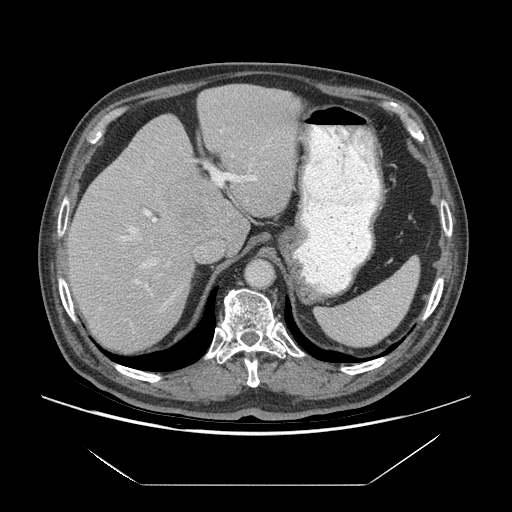
Contrast-enhanced abdominal CT (liver protocol), one axial slice. Slice 48 of 75 in the series (ordered by position). Reconstruction kernel STANDARD. 140 kVp. Soft-tissue window (W 400 / L 40 HU). 2.5 mm slice thickness. 512 × 512 image matrix. From the clinical record (not read from this slice): diagnosis: hepatocellular carcinoma (patient treated with transarterial chemoembolisation; whether this scan precedes or follows treatment is not stated here); TNM stage (as recorded): Stage-I; Child-Pugh class: A; tumour differentiation: well differentiated; tumour nodularity: uninodular.
Structures marked on this image (semi-automatically segmented with operator editing):
- liver parenchyma outside the tumour (the mass and vessels are separate outlines, so this box may not span the whole liver): bounding box <66,84,300,352> (left, top, right, bottom; pixels)
- mass: <164,174,219,232>
- liver vessels: <119,130,272,305>